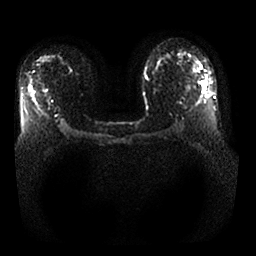
Breast MRI, one axial slice; slice 19 of 25 in the series (ordered by position); diffusion-weighted series; image 2 of 4 stored at this slice position (different b-values; order by instance number); 1.5 T; 4 mm slice thickness; 256 × 256 image matrix. Female patient.
Structures marked on this image (manually delineated by an expert):
- tumour on diffusion-weighted imaging: bounding box [x1, y1, x2, y2] px = [201, 81, 206, 86]